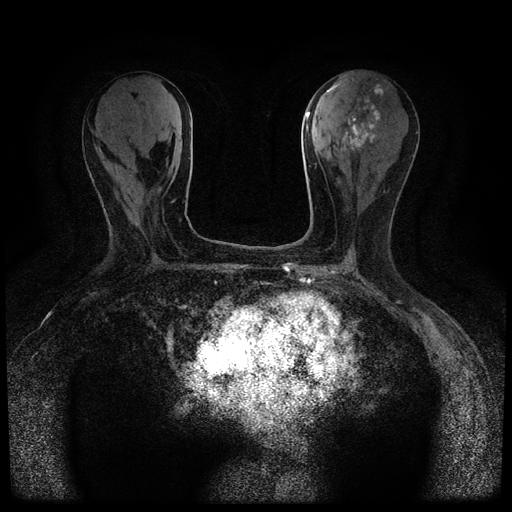
Breast MRI (dynamic contrast-enhanced, multi-phase), one axial slice. Slice 34 of 116 in the series (ordered by position). Dynamic contrast-enhanced series, time point 2 of 5 at this slice position (early post-contrast). 1.5 T. TE 2.7 ms, TR 5.4 ms. 512 × 512 image matrix. Female patient, age 80 years.
Structures marked on this image (semi-automatically segmented with operator editing):
- breast lesion (labelled 'tumour' in the annotation; benign lesions carry a separate 'benign' label): box from (x=342, y=84) to (x=384, y=151) px